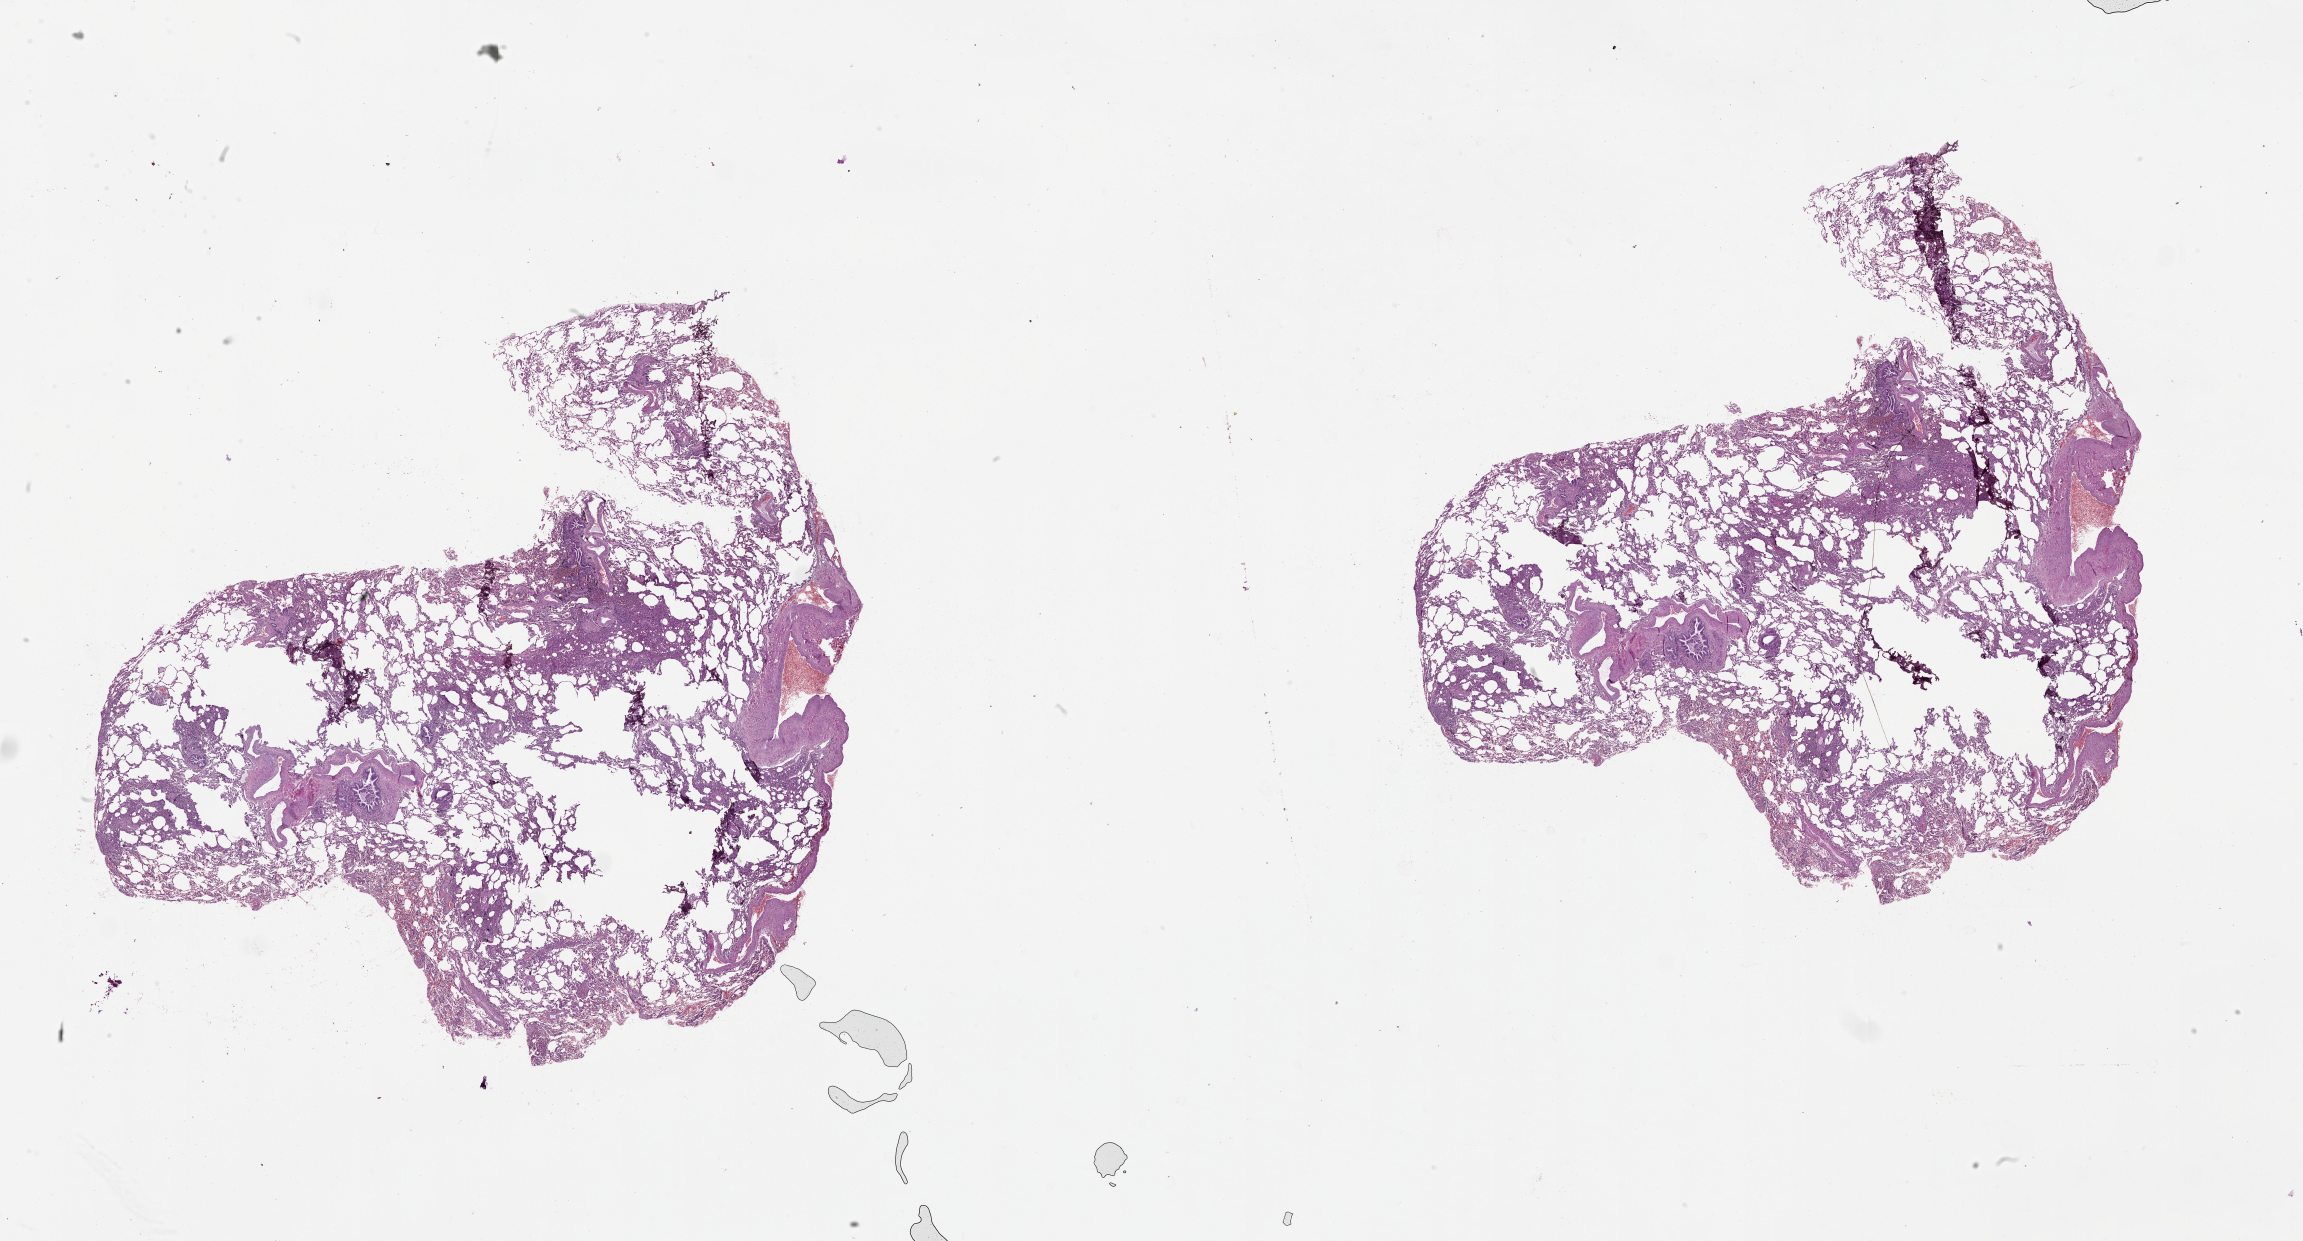
H&E whole-slide image — a low-resolution overview of the entire scanned area, about 37.1 x 20.0 mm; normal (non-tumour) tissue sample, lung. 53-year-old male patient.
This section: normal (non-tumour) tissue from the same patient. Patient diagnosis (cohort enrolment): squamous cell carcinoma (lung).